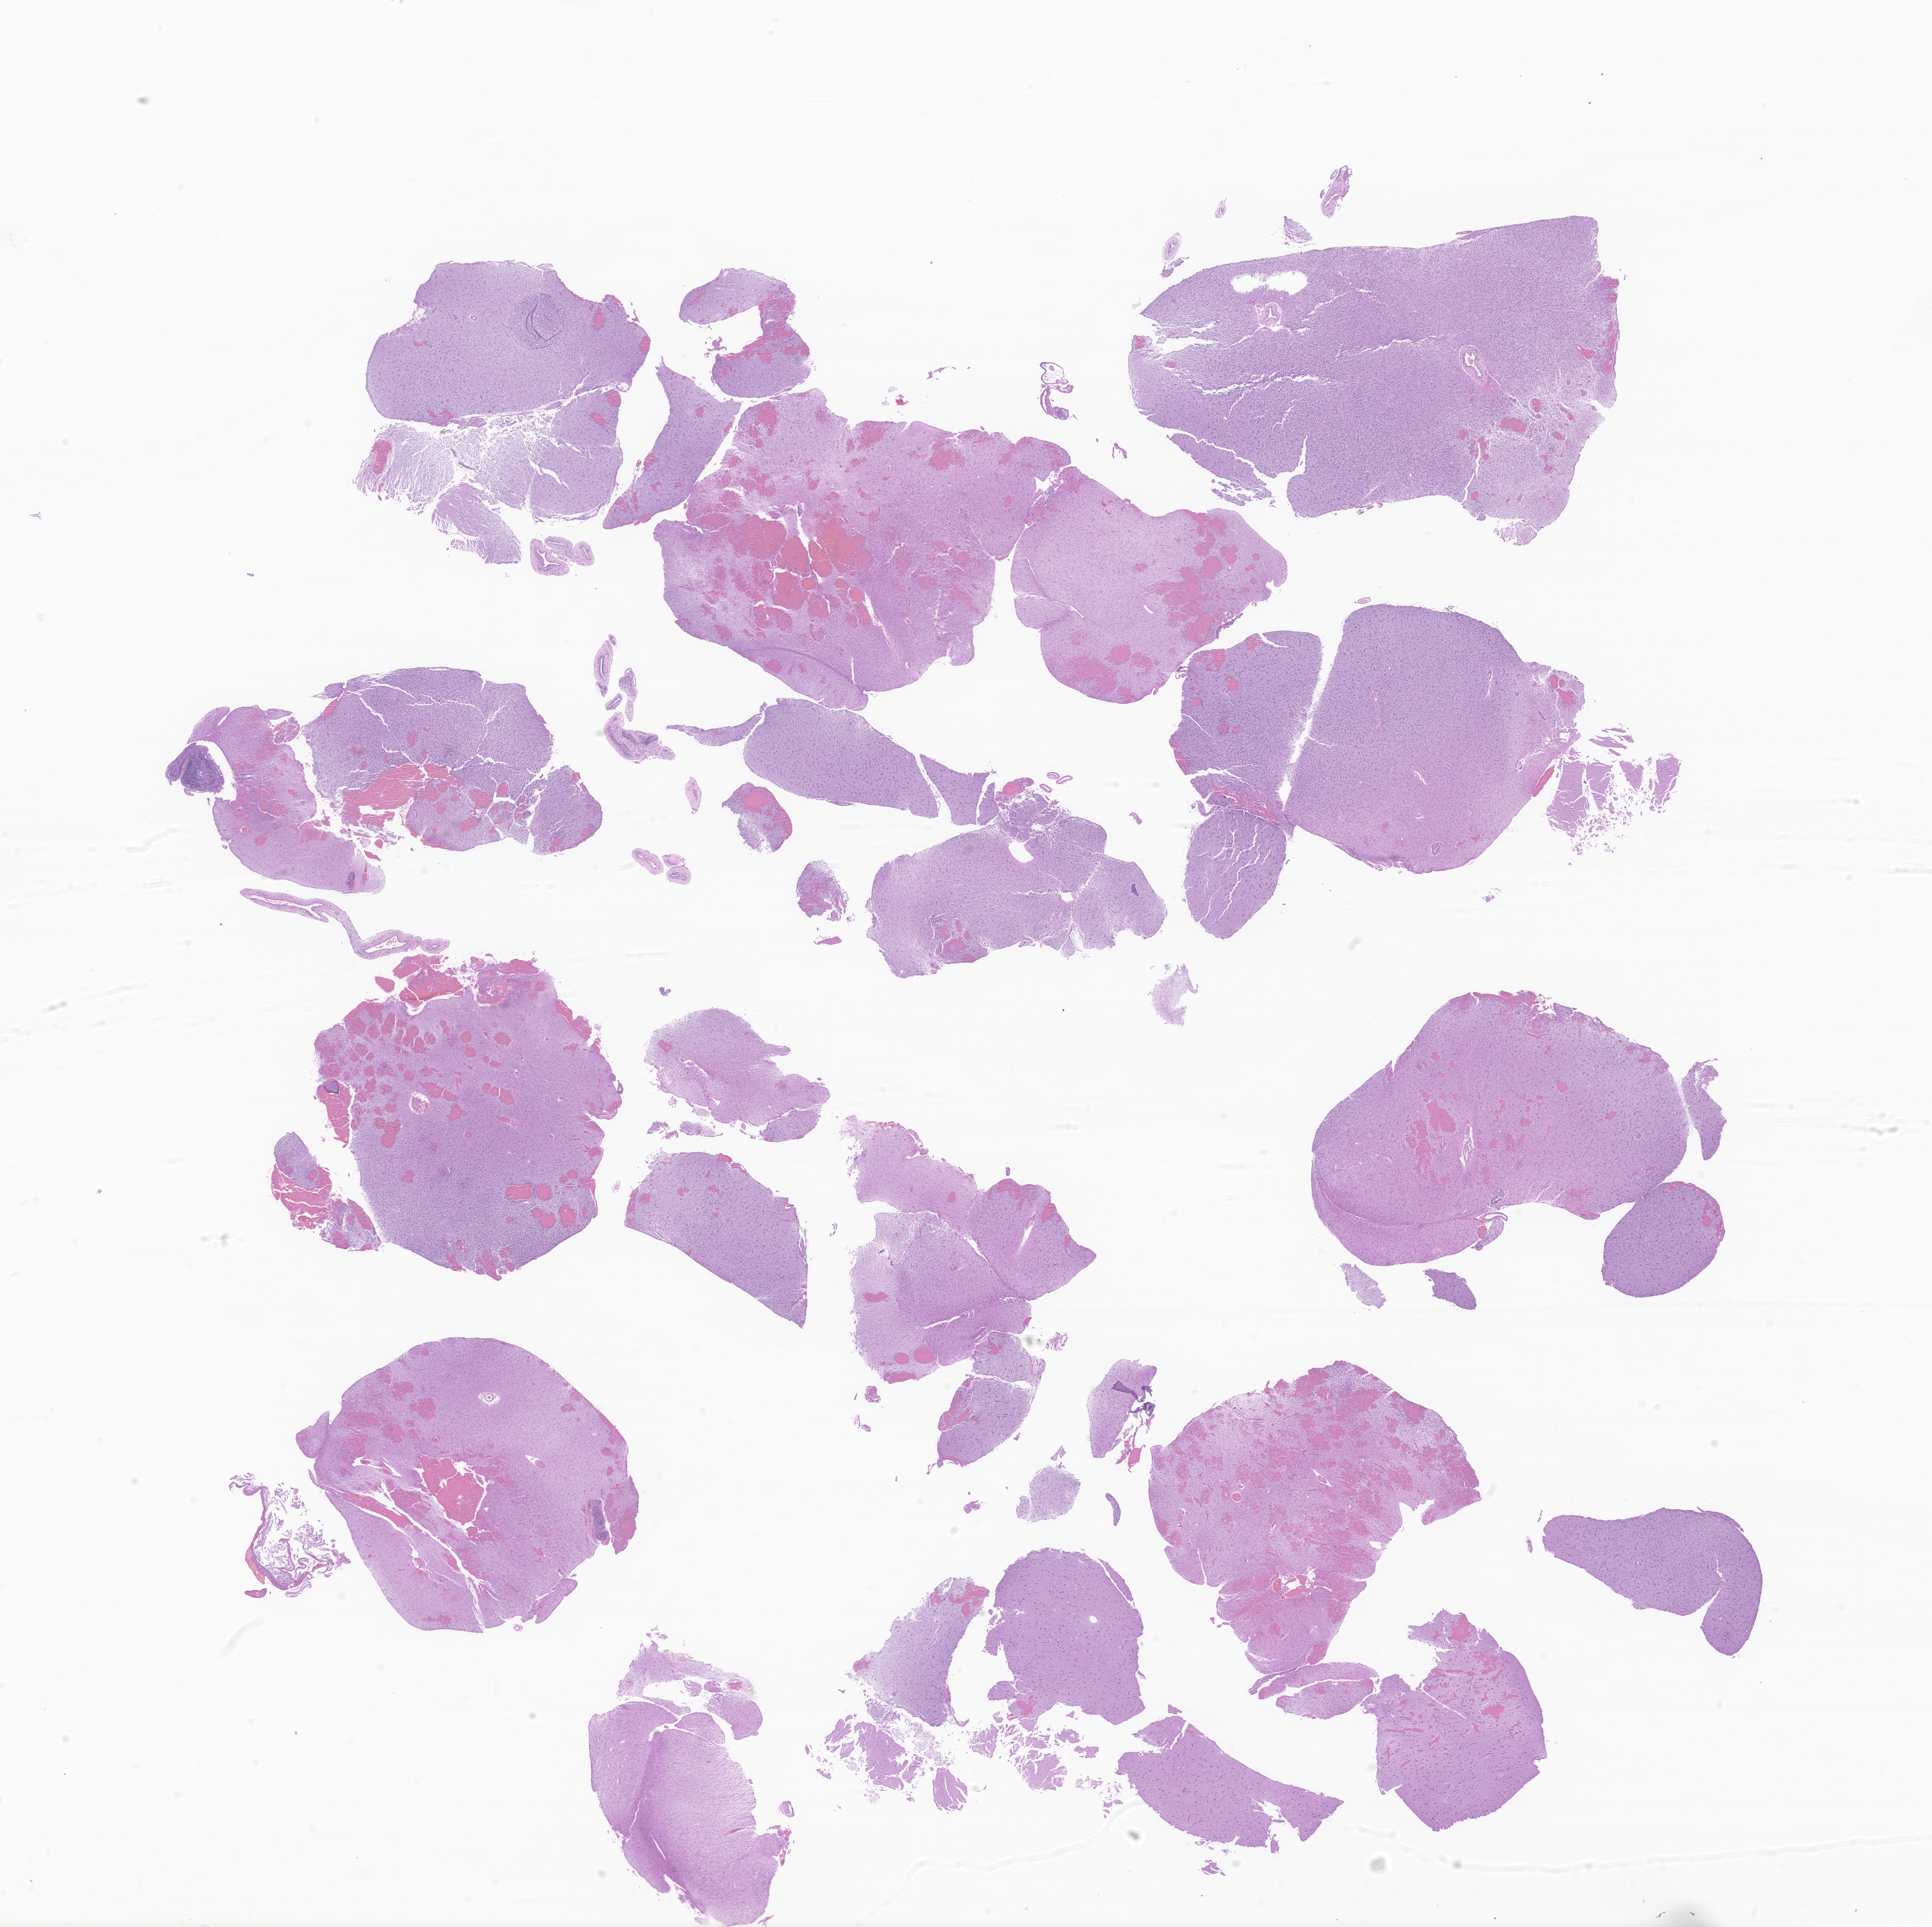
Digitized hematoxylin and eosin (H&E)-stained section of tumor tissue from the brain, shown as a low-resolution overview of the whole scanned area (about 21.3 x 21.2 mm). Formalin-fixed paraffin-embedded section. Patient female; age 175 months (14 years 7 months).
Recorded diagnosis: Oligodendroglioma, NOS.